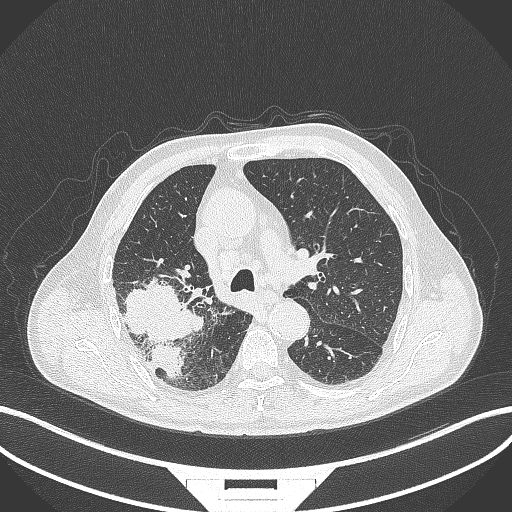
Chest CT, one axial slice; slice 275 of 429 in the series (ordered by position); reconstruction kernel B70f; 120 kVp; lung window (W 1500 / L -600 HU); 512 × 512 image matrix. Patient: male, 72 years. Case-level facts recorded for this patient, not image findings: clinical TNM (as recorded): T3 N2 M0.
Annotated regions visible in this slice (bounding box drawn by a radiologist):
- lung tumour (recorded histology: adenocarcinoma): box from (x=119, y=278) to (x=204, y=384) px